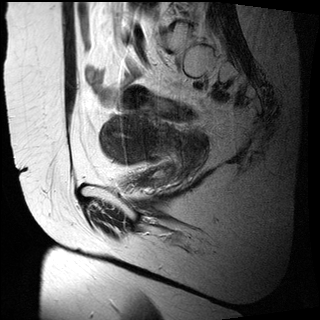
Pelvic MRI for cervical cancer, one sagittal slice; slice 19 of 27 in the series (ordered by position); T2-weighted; 1.5 T; TE 89 ms, TR 2740 ms; 4 mm slice thickness; 320 × 320 image matrix, field of view 260 × 260 mm. Female patient, age 47 years.
Structures marked on this image (outlined manually by an expert reader):
- uterus and cervix: bounding box [x1, y1, x2, y2] px = [99, 115, 209, 168]